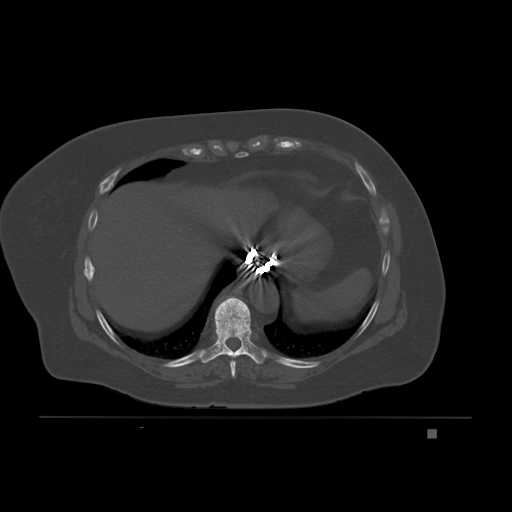
CT including the spine, one axial slice; bone window (W 1800 / L 400 HU); 3 mm slice thickness; 512 × 512 image matrix, field of view 474 × 474 mm. Patient: female, 63 years. From the clinical record (not read from this slice): primary cancer: breast.
Annotated regions visible in this slice (semi-automatically segmented with operator editing):
- T8 vertebra: bounding box <229,360,237,378> (left, top, right, bottom; pixels)
- T9 vertebra: <201,296,265,364>